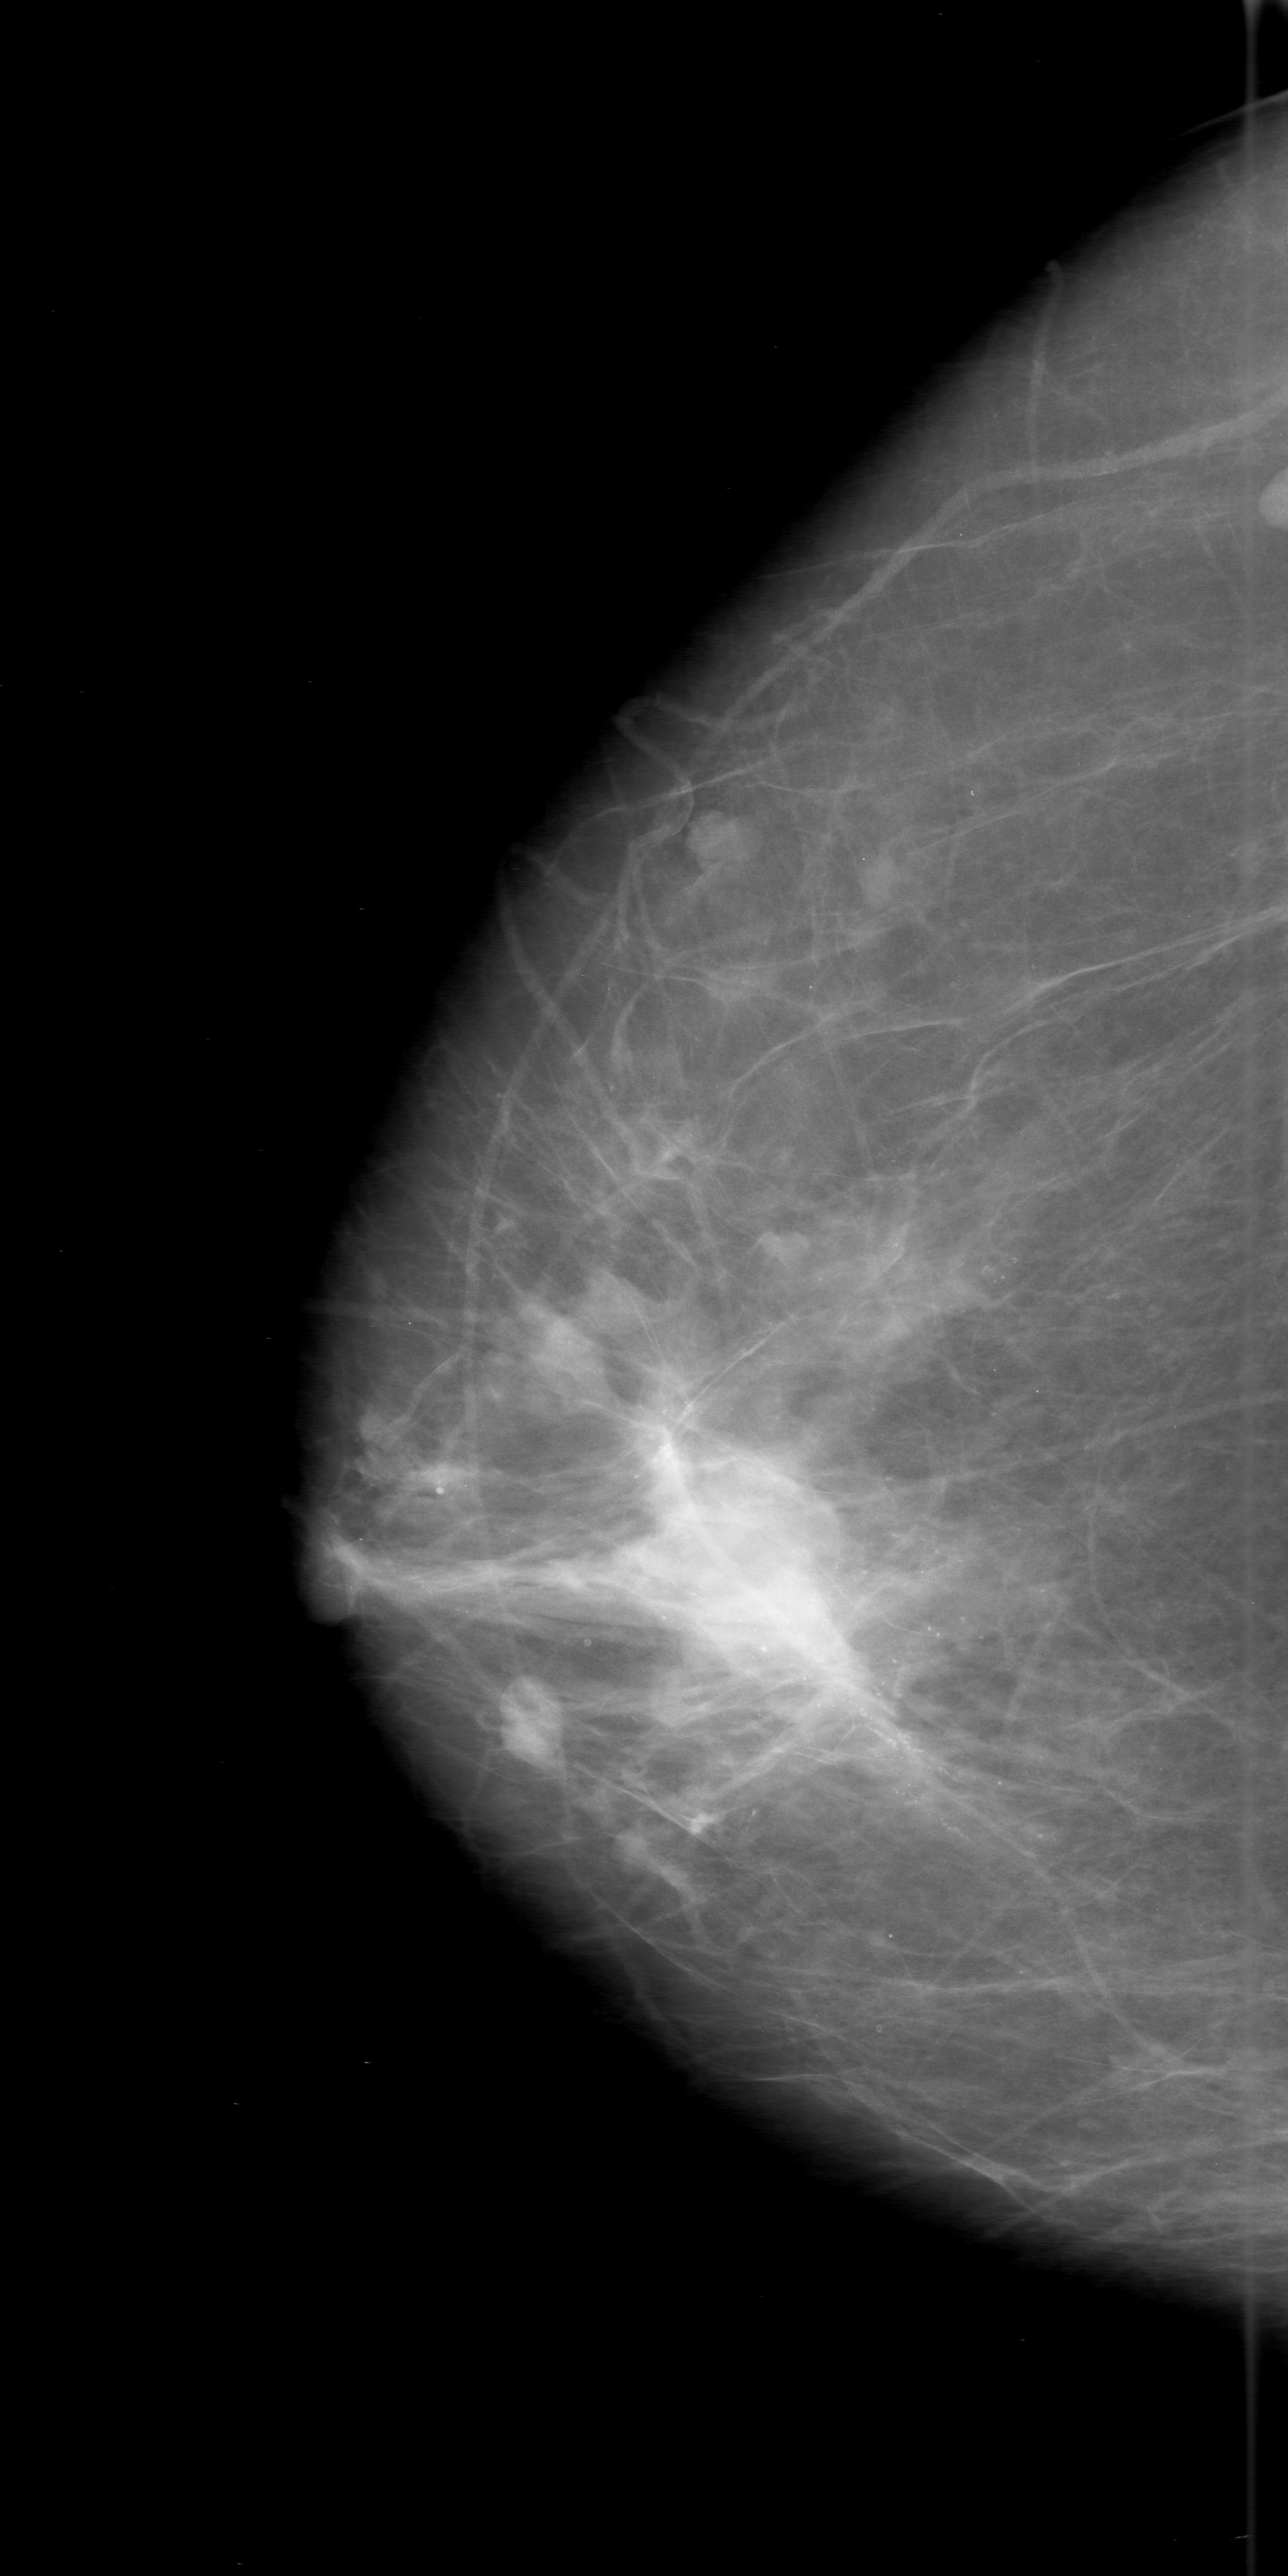
Scanned film-screen mammogram, right breast, craniocaudal (CC) view, breast composition: scattered fibroglandular densities (BI-RADS density category 2 of 4).
- Finding: calcifications, morphology amorphous / pleomorphic, distribution segmental; BI-RADS assessment category 5; pathology result (as recorded, not read from the image): malignant.